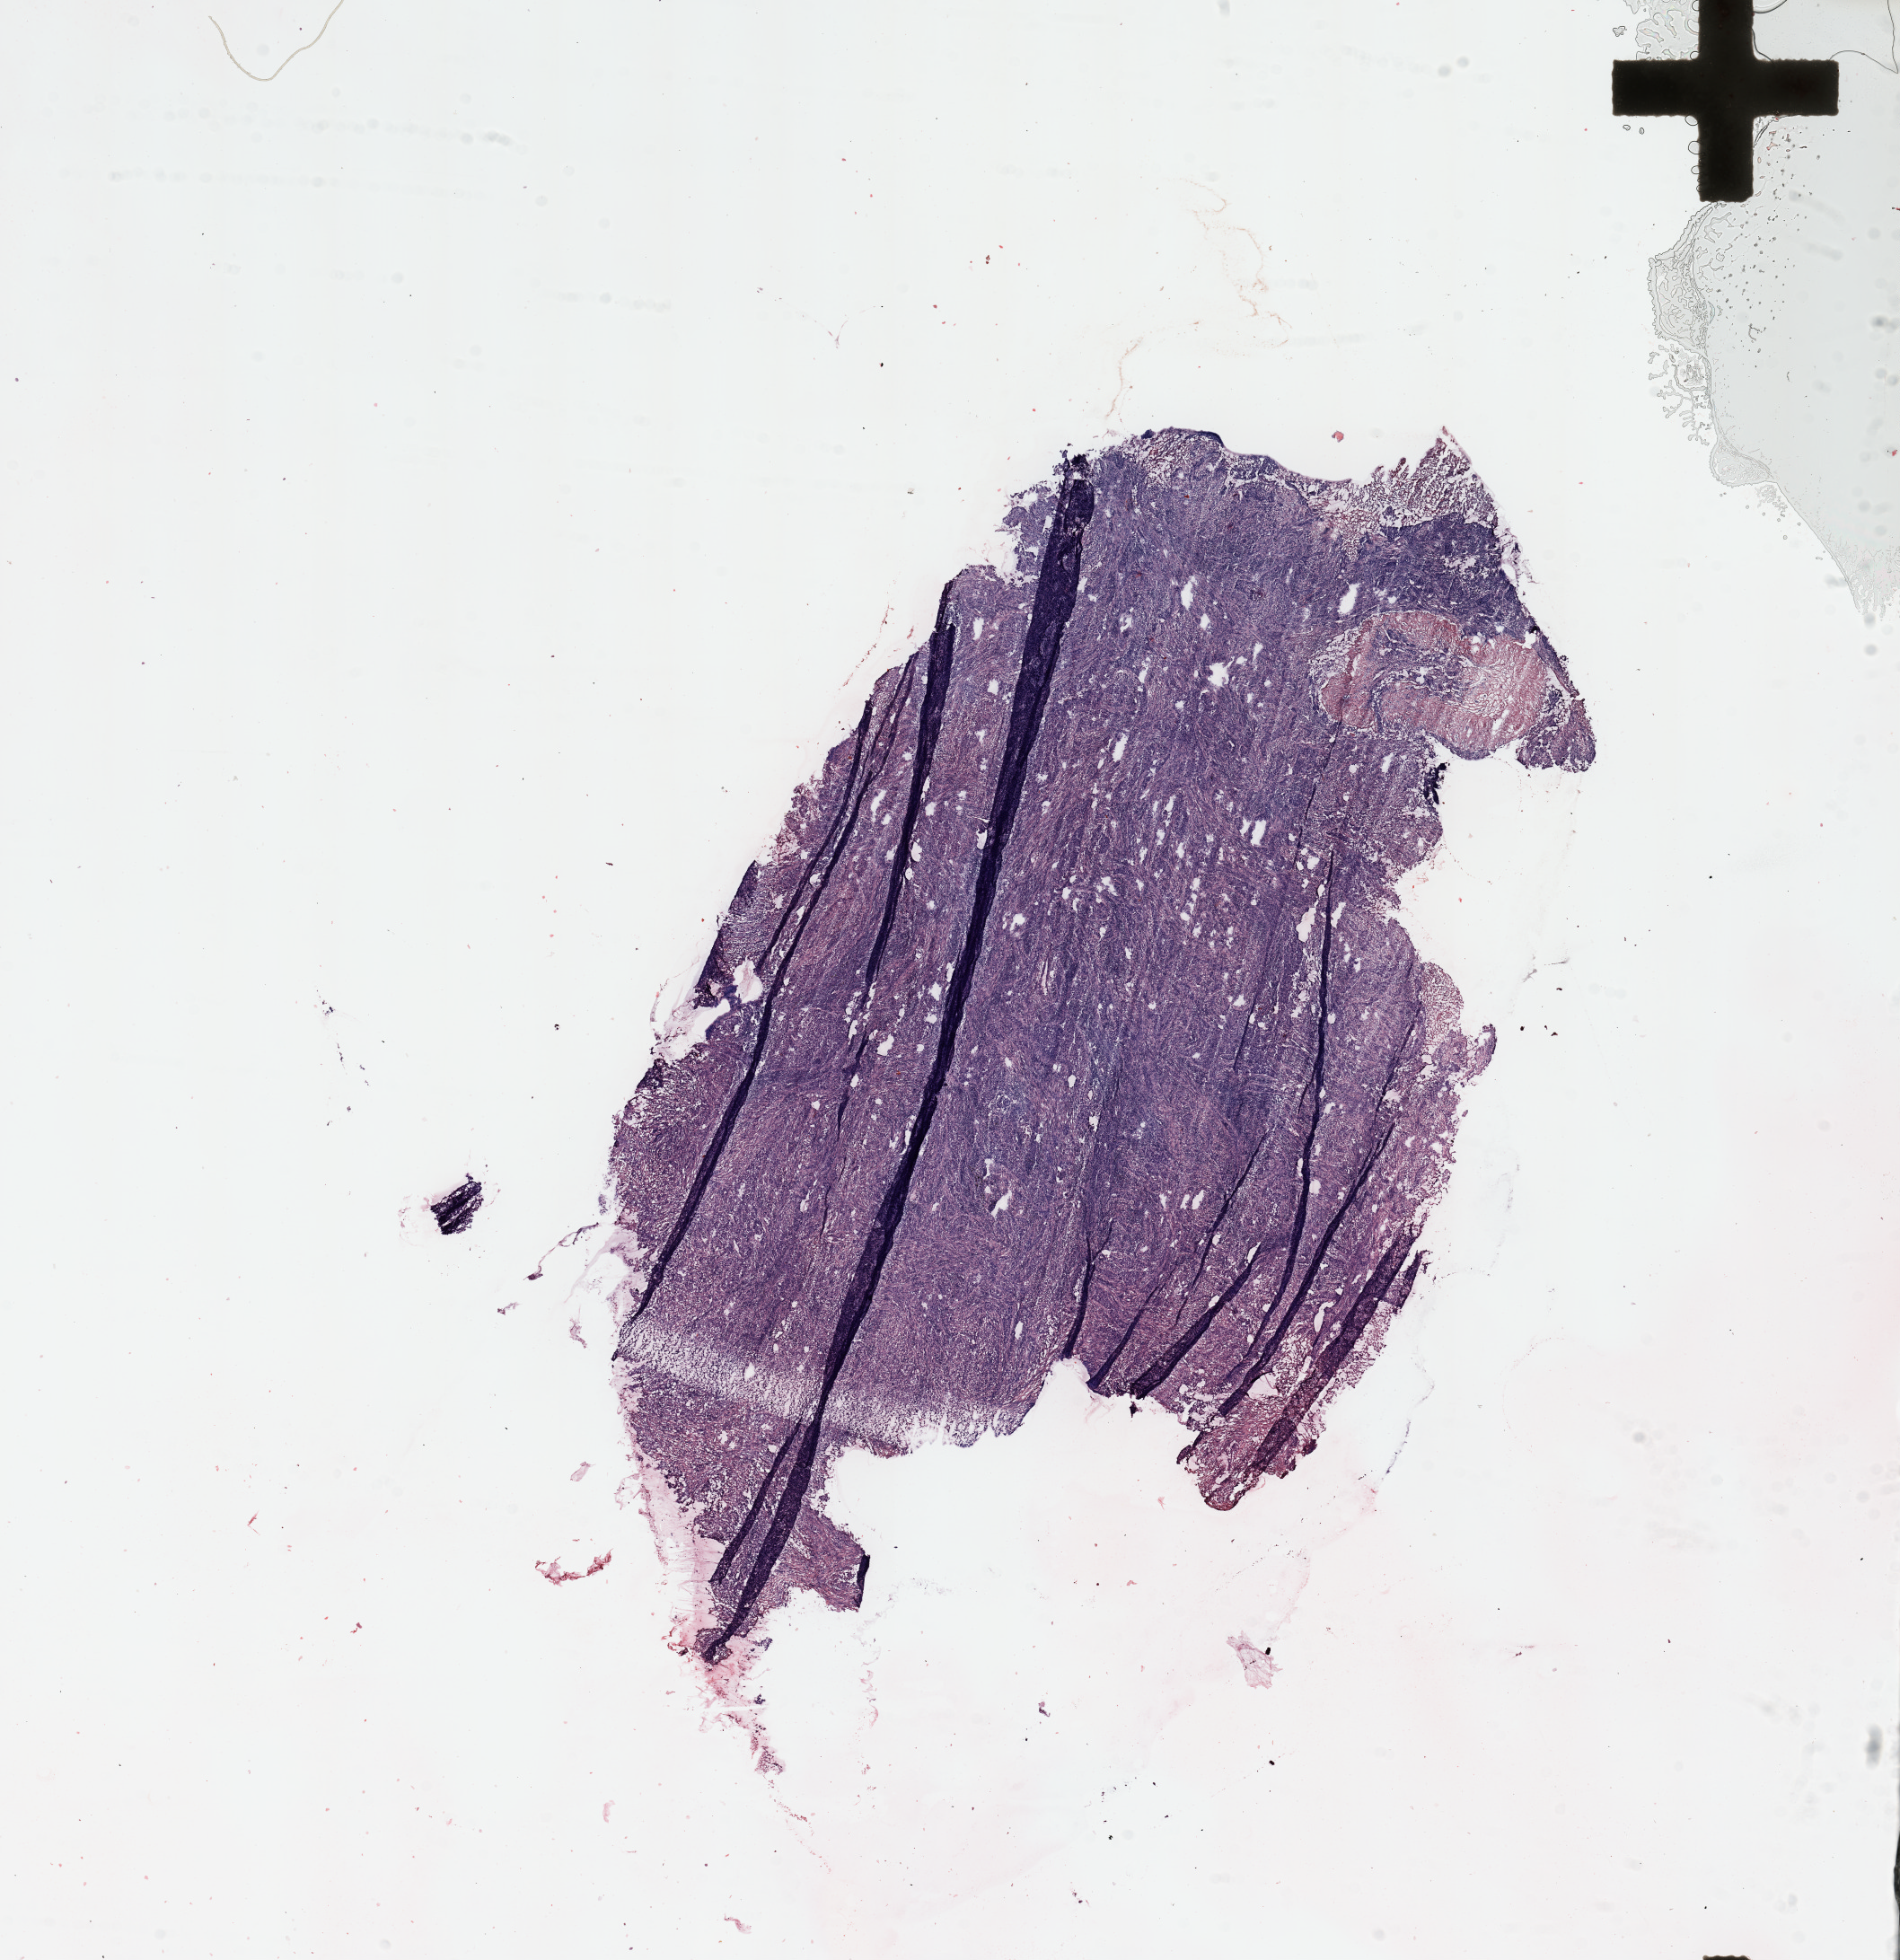
Whole-slide histology image, H&E — low-resolution overview of the scanned area, about 16.7 x 17.3 mm (from a 20x scan); tumour tissue sample, lung. Male, 67 y/o.
Primary tumour site (as recorded): left upper lobe. Patient diagnosis (cohort enrolment): squamous cell carcinoma (lung).